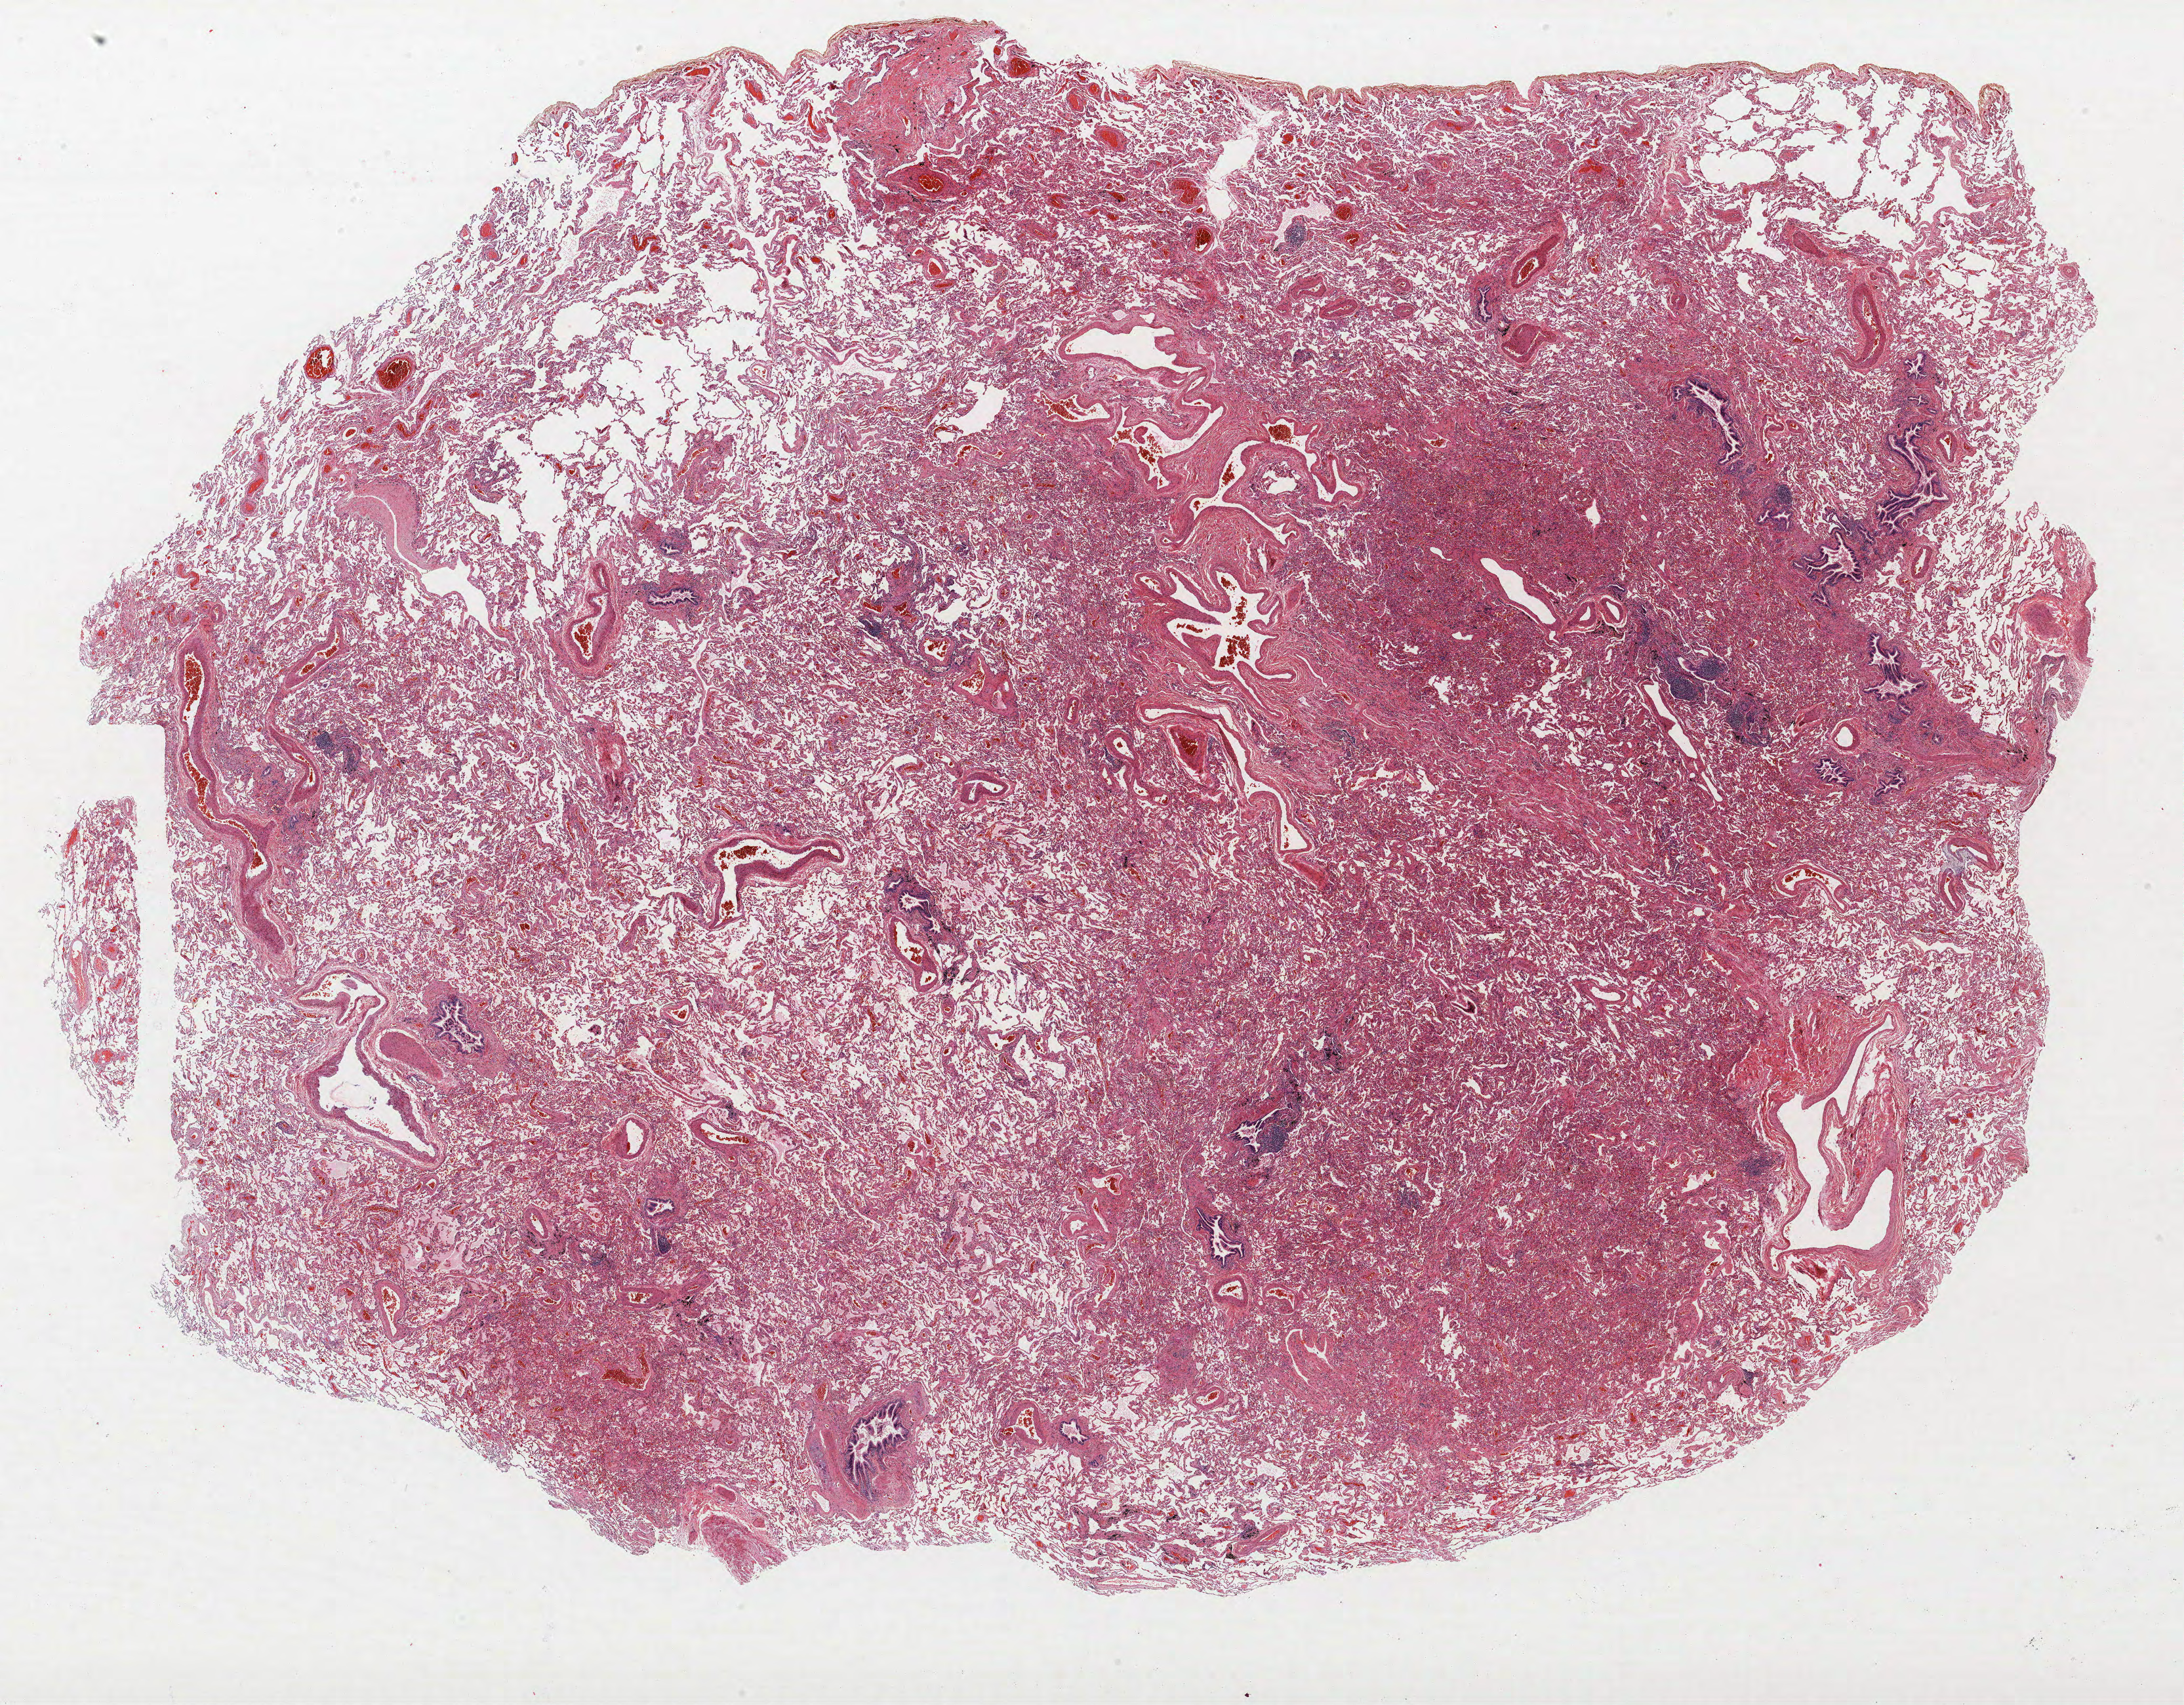
Whole-slide histology image, Hematoxylin and eosin (H&E) stained — a low-resolution overview of the entire scanned area, about 26.6 x 20.8 mm, FFPE section, lung. Female, age 58 at enrolment. Grade: poorly differentiated (G3).
• stage (AJCC 6th edition): IIIA
• participant's lung-cancer diagnosis: Acinar cell carcinoma
• ICD-O-3 topography: upper lobe of lung (C34.1)
• tumour size (pathology): 37 mm
• primary tumour location (clinical record): left upper lobe